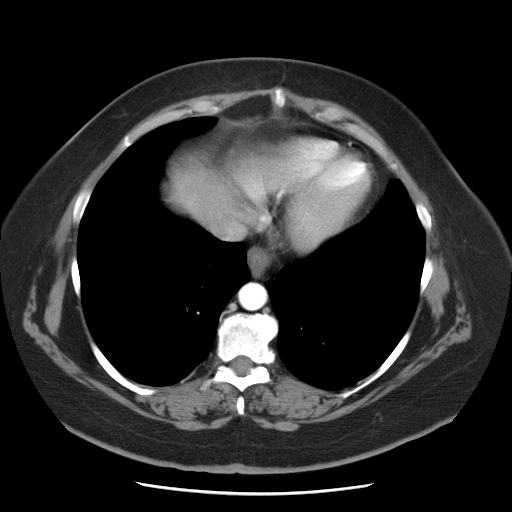
Contrast-enhanced abdominal CT, one axial slice. Slice 44 of 55 in the series (ordered by position). Reconstruction kernel STANDARD. Intravenous contrast given. Soft-tissue window (W 400 / L 40 HU). 5 mm slice thickness. 512 × 512 image matrix, field of view 380 × 380 mm. Female patient, age 52 years. From the clinical record (not read from this slice): diagnosis: colorectal cancer liver metastases, imaged before liver resection.
Outlined on this slice (outlined manually by an expert reader):
- liver: box from (x=160, y=149) to (x=260, y=230) px